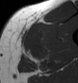
MRI of an extremity soft-tissue mass, one axial slice; MR volume resampled by the dataset authors to the PET/CT grid (not the native acquisition matrix); 3.27 mm slice thickness; 78 × 83 image matrix. Male patient. Case-level facts recorded for this patient, not image findings: histological type: pleiomorphic leiomyosarcoma; grade: high; site of the primary tumour: left thigh.
Annotated regions visible in this slice (expert contour drawn on MRI and transferred to this co-registered scan by the dataset authors):
- gross tumour volume including surrounding oedema: bounding box [x1, y1, x2, y2] px = [20, 24, 46, 59]
- gross tumour volume (mass): [25, 35, 42, 59]